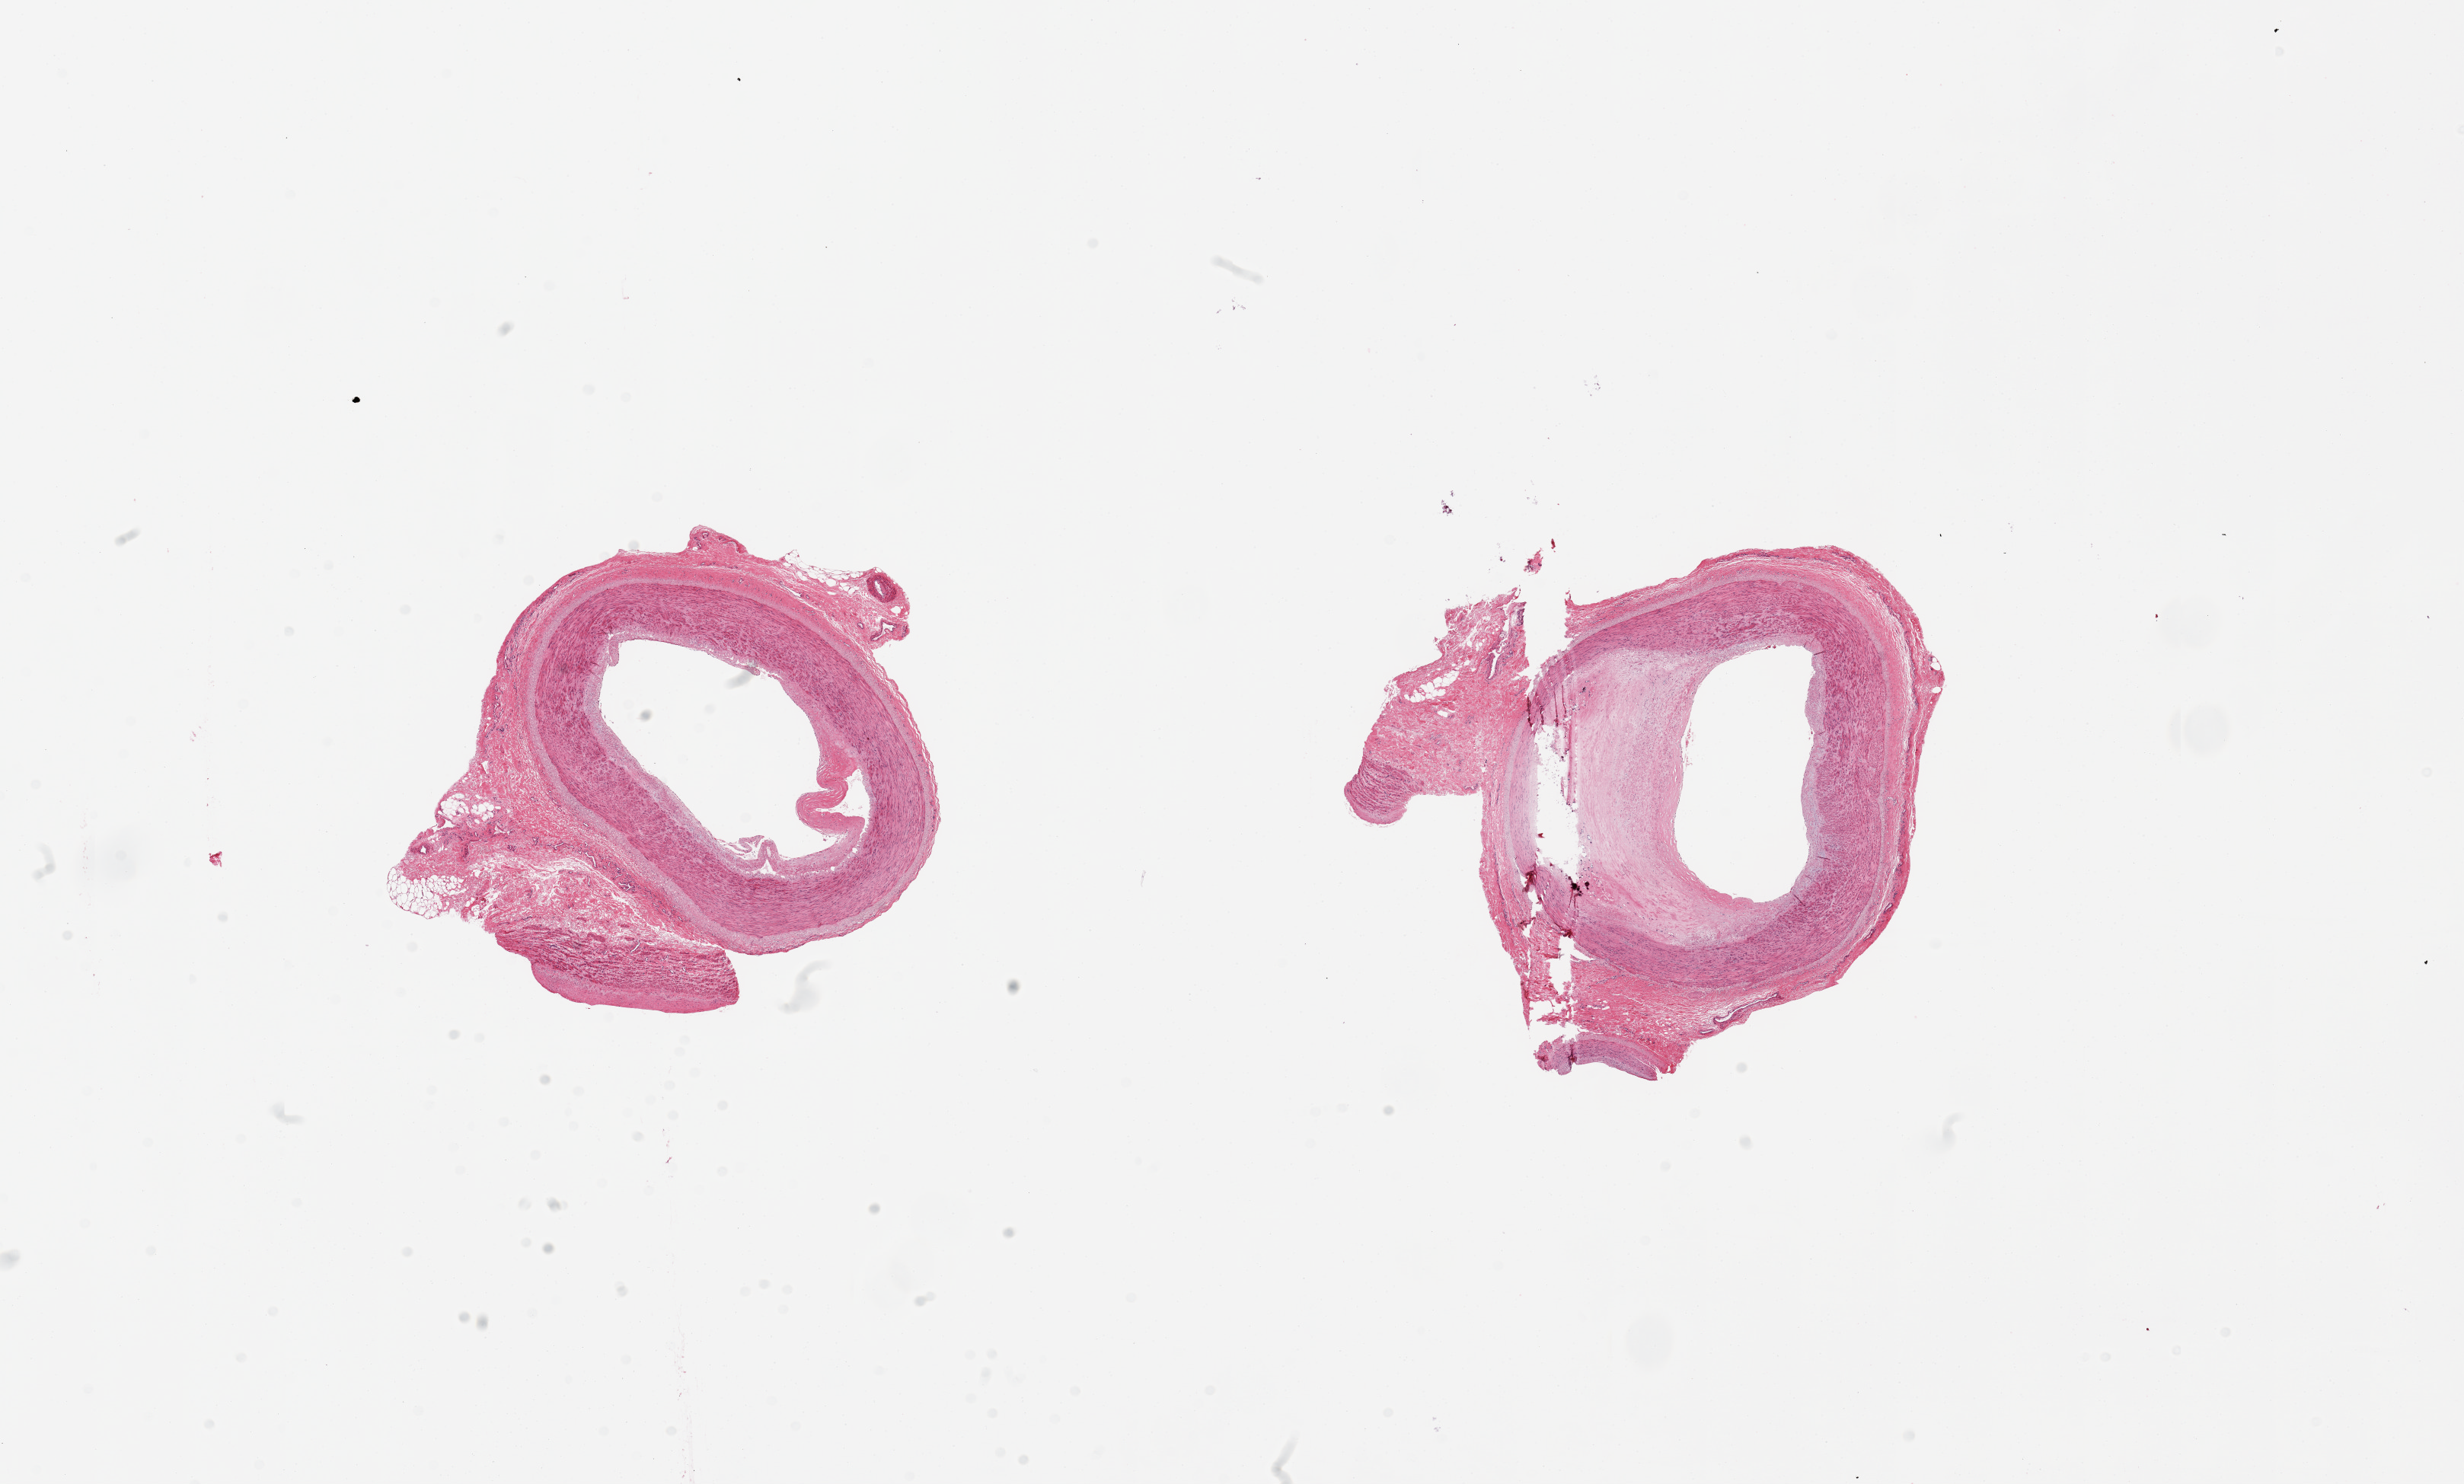
Haematoxylin and eosin whole-slide image, shown as a low-resolution overview of the whole scanned area (about 25.6 x 15.4 mm). PAXgene-fixed, paraffin-embedded tissue. Target tissue: tibial artery. Tissue donor sample. Donor sex: male.
Pathologist's review note for this sample: 2 pieces, 6x5 & 6x6mm. 1 with 50% occlusive fibrocalcific plaque; 1x2mm extraneous fibroadipose tissue.